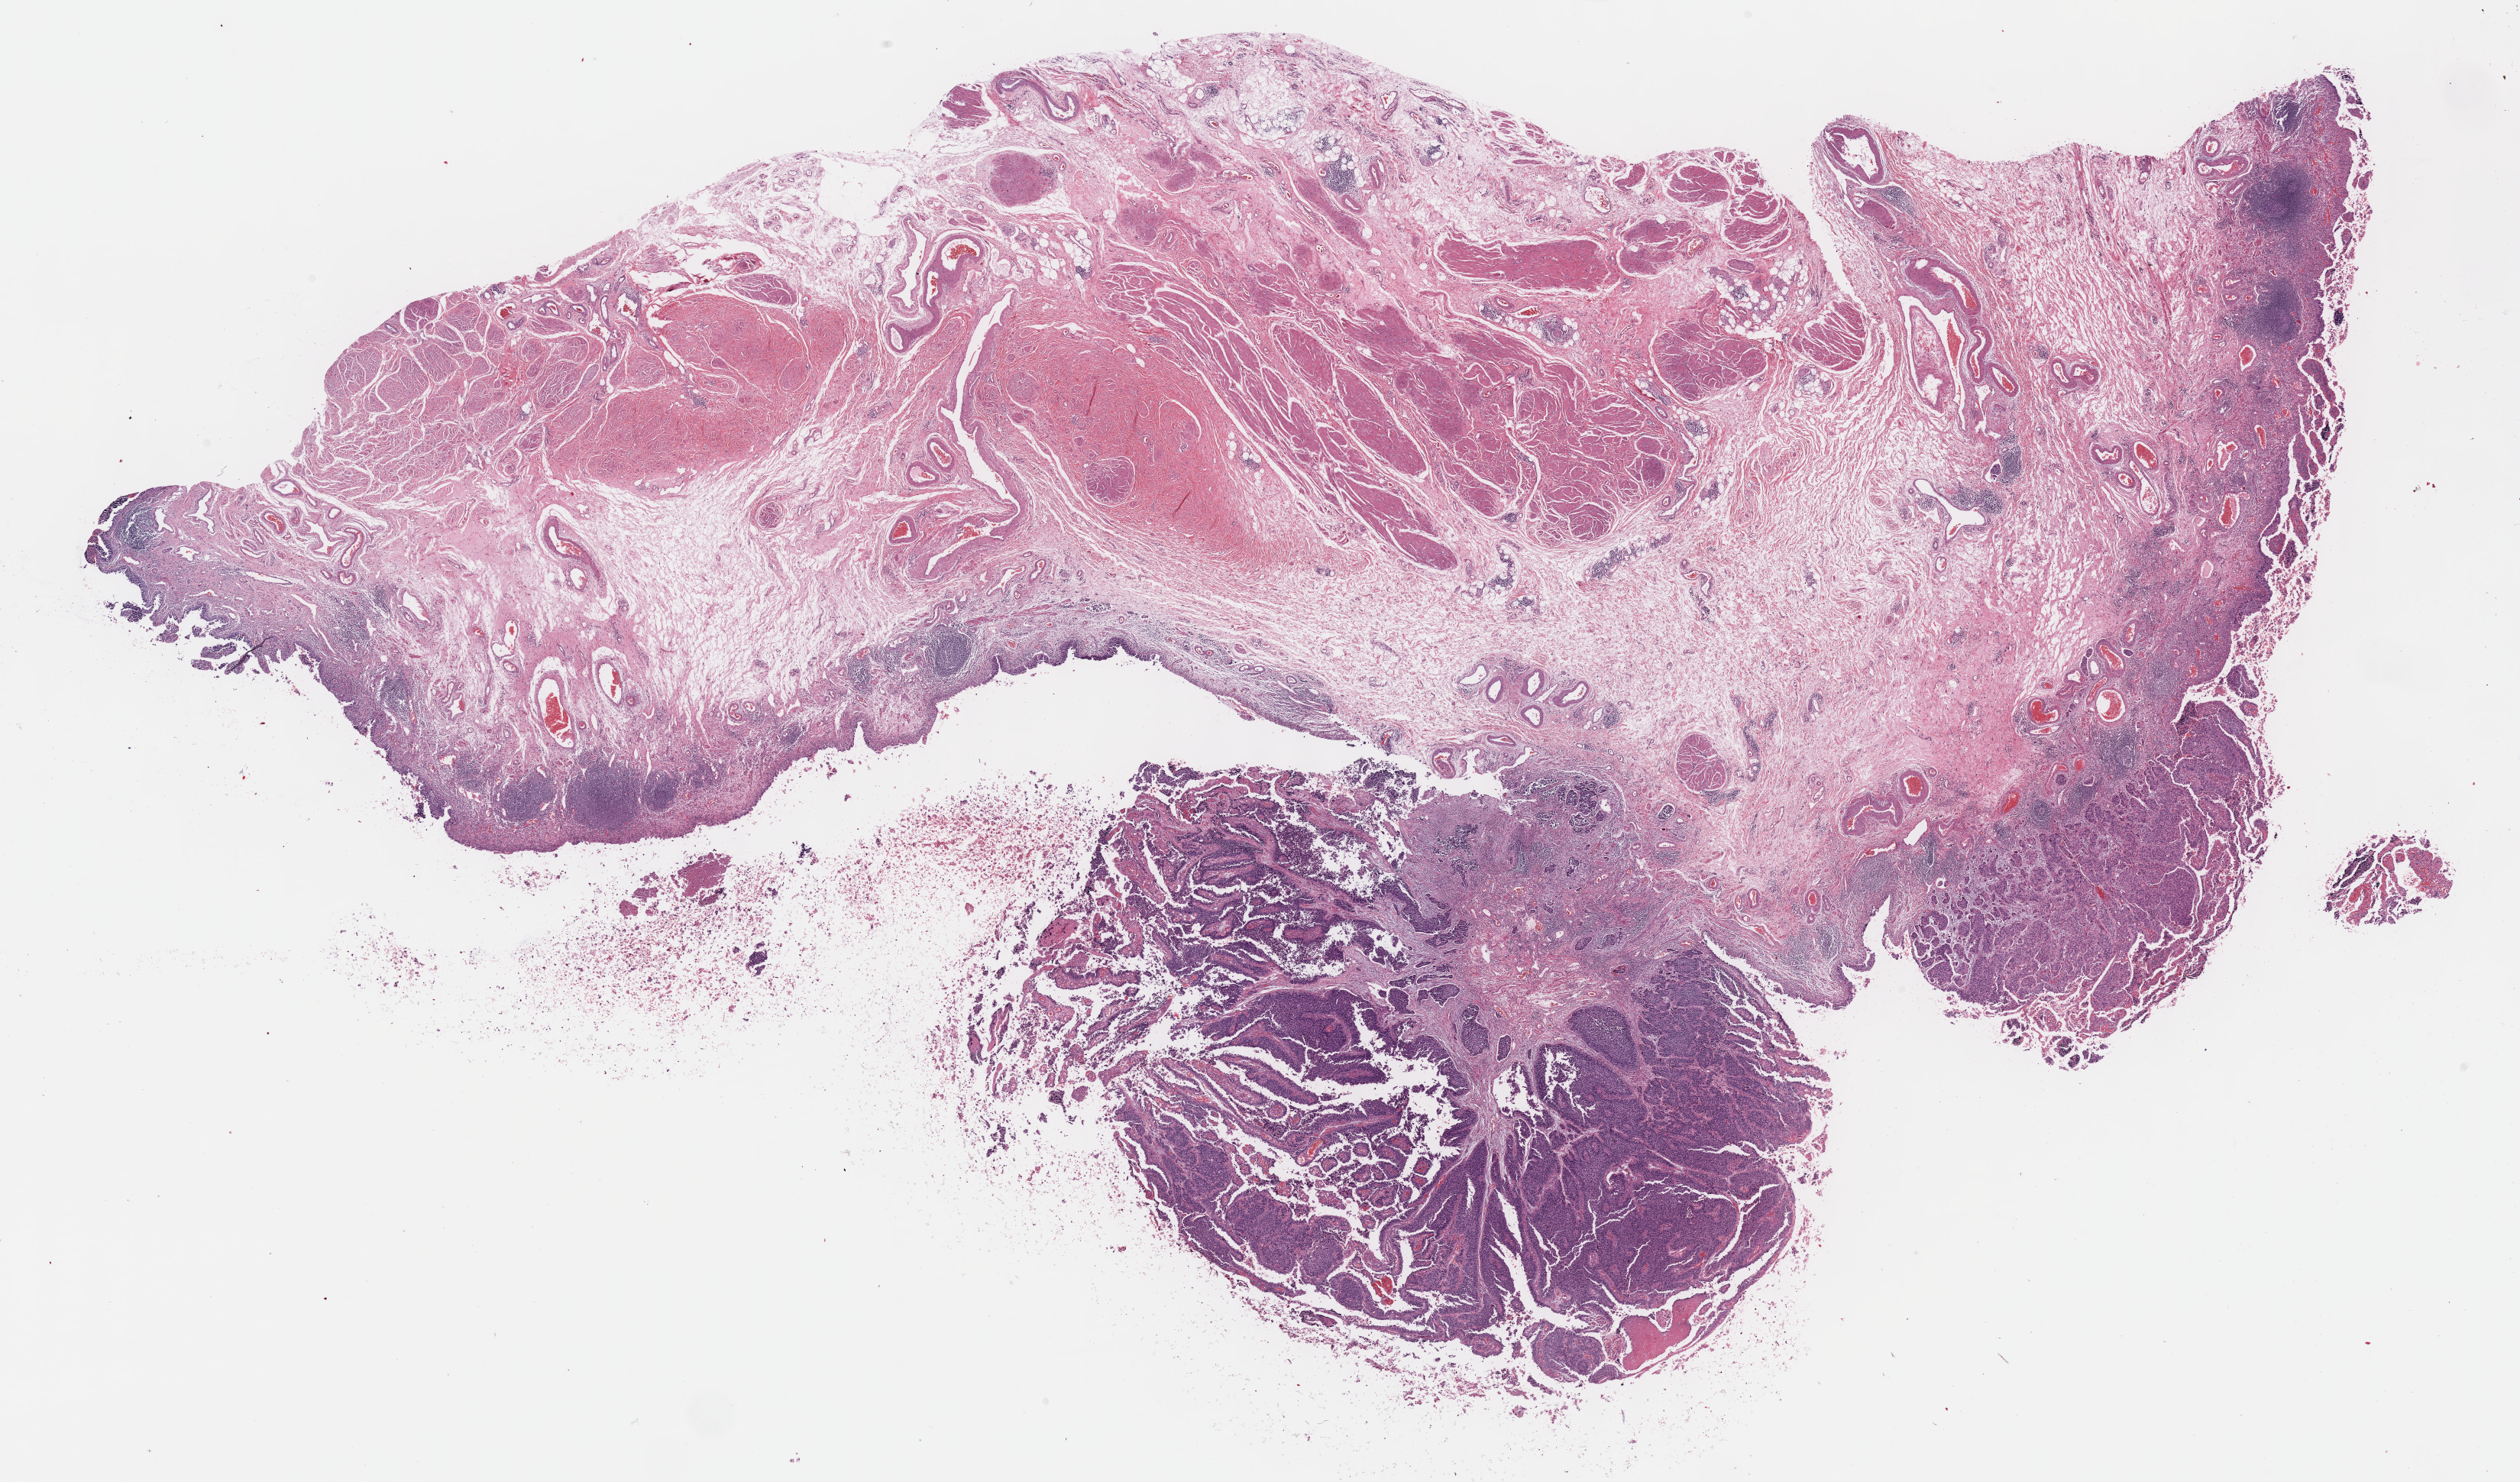
Whole-slide histology image, H&E-stained — shown as a low-resolution overview of the whole scanned area (about 26.7 x 15.7 mm); FFPE section; primary tumour sample from the bladder. Female, age 81 years at initial diagnosis. Histologic grade: high grade.
* histologic diagnosis: Papillary transitional cell carcinoma
* AJCC pathologic stage: IV
* lymph nodes positive (case pathology): 5 of 69 examined